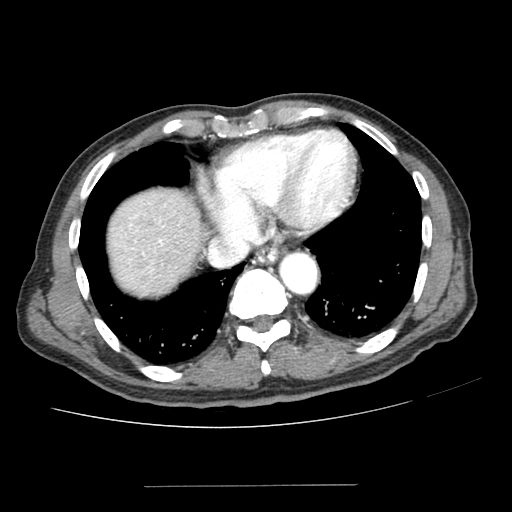
Contrast-enhanced abdominal CT (liver protocol), one axial slice. Slice 178 of 187 in the series (ordered by position). Reconstruction kernel SOFT. One of 2 acquisitions stored at this slice position. Soft-tissue window (W 400 / L 40 HU). 2.5 mm slice thickness. 512 × 512 image matrix, field of view 360 × 360 mm. From the clinical record (not read from this slice): diagnosis: hepatocellular carcinoma (patient treated with transarterial chemoembolisation; whether this scan precedes or follows treatment is not stated here); TNM stage (as recorded): Stage-I; Child-Pugh class: A; tumour differentiation: poorly differentiated.
Structures marked on this image (semi-automatic segmentation, software-assisted and operator-edited):
- abdominal aorta: bounding box <280,253,317,293> (left, top, right, bottom; pixels)
- liver parenchyma outside the tumour (the mass and vessels are separate outlines, so this box may not span the whole liver): <108,188,206,295>
- liver vessels: <130,217,163,245>